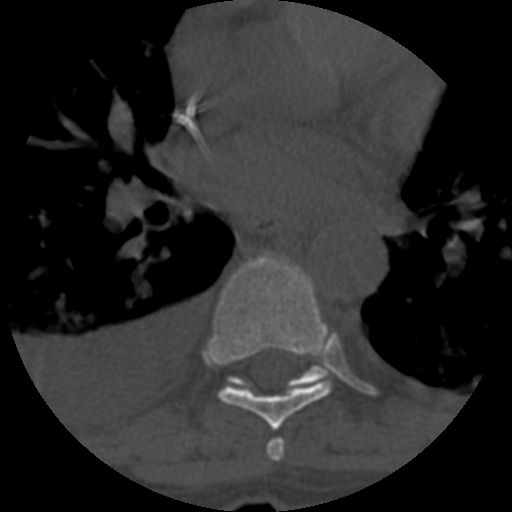
CT including the spine, one axial slice. Position 412 of 708 along the scan axis. Reconstruction kernel STANDARD. 120 kVp. One of 3 acquisitions stored at this slice position. Bone window (W 1800 / L 400 HU). 512 × 512 image matrix, field of view 160 × 160 mm. Patient age 55 years. From the clinical record (not read from this slice): primary cancer: colon.
Structures marked on this image (semi-automatically segmented with operator editing):
- T6 vertebra: bounding box (x1, y1, x2, y2) in pixels: (266, 438, 285, 461)
- T7 vertebra: (211, 253, 332, 430)
- T8 vertebra: (228, 365, 328, 390)